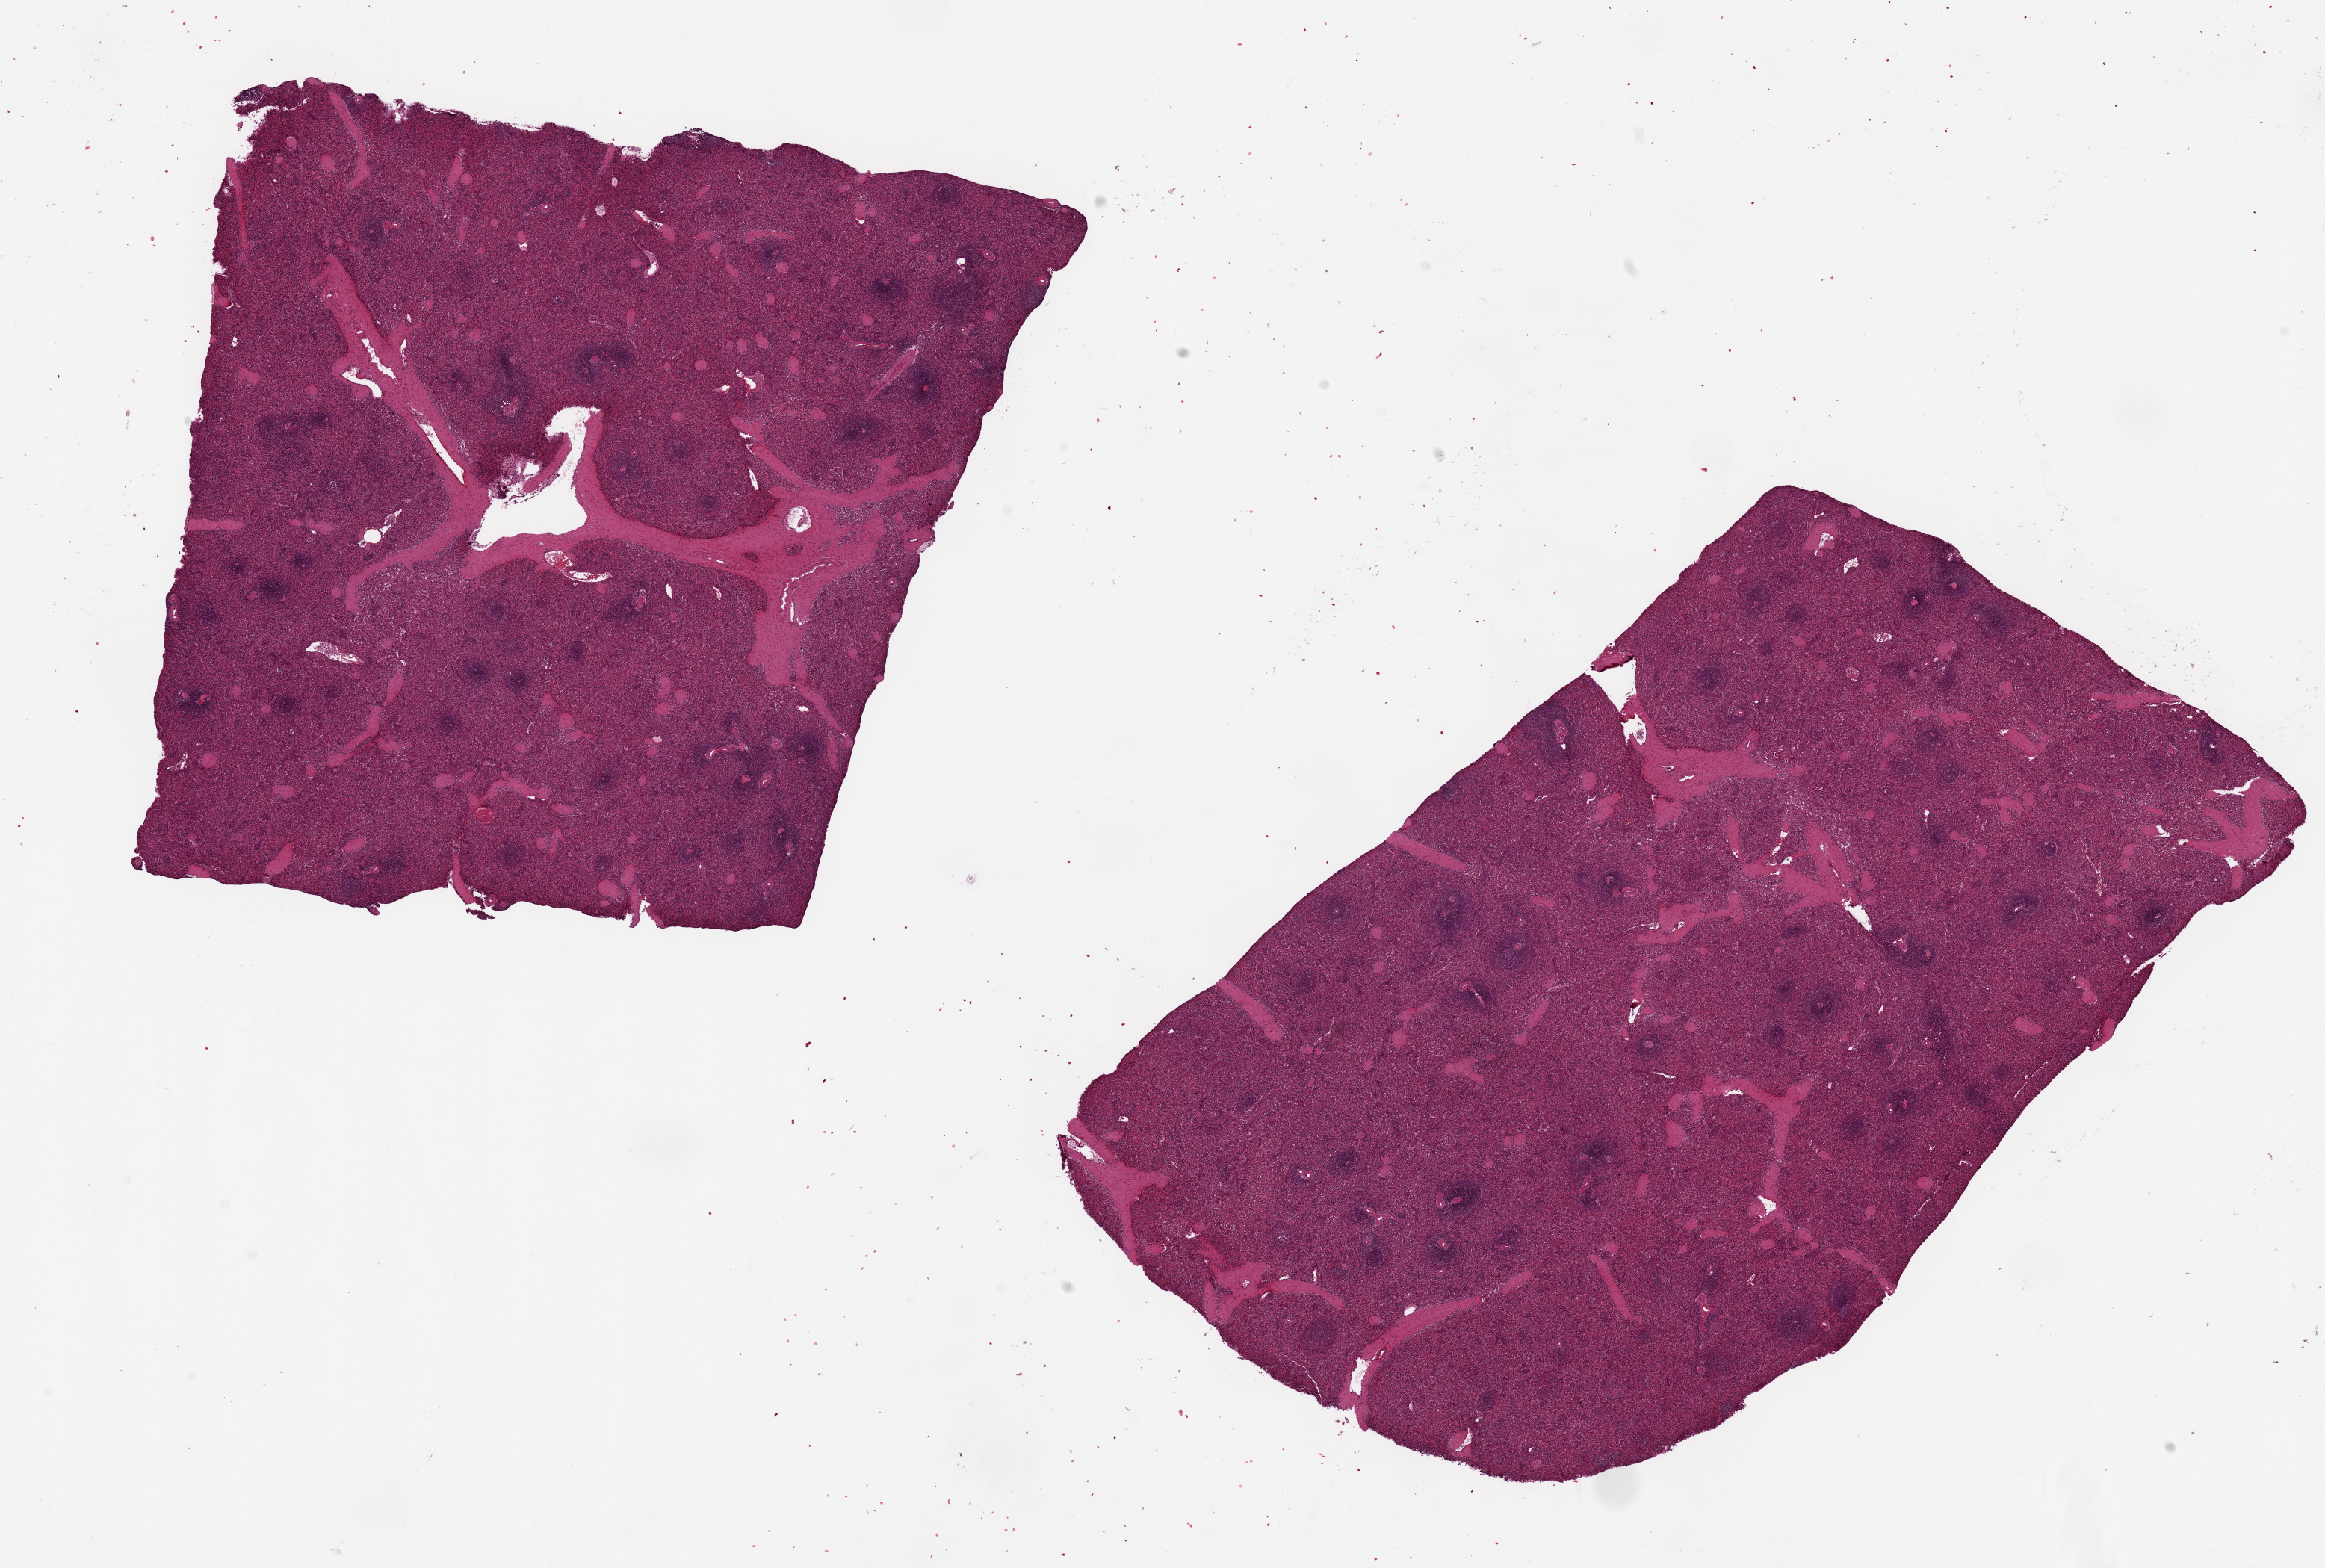
Digitized haematoxylin and eosin-stained section, brightfield, a low-resolution overview of the entire scanned area, about 24.6 x 16.6 mm. PAXgene-fixed paraffin-embedded (PFPE) section. Sampled site (target tissue): spleen. Donor tissue sample. Donor: male.
• pathologist's review note for this sample: 2 pieces 11x7 & 8x8; no congestion